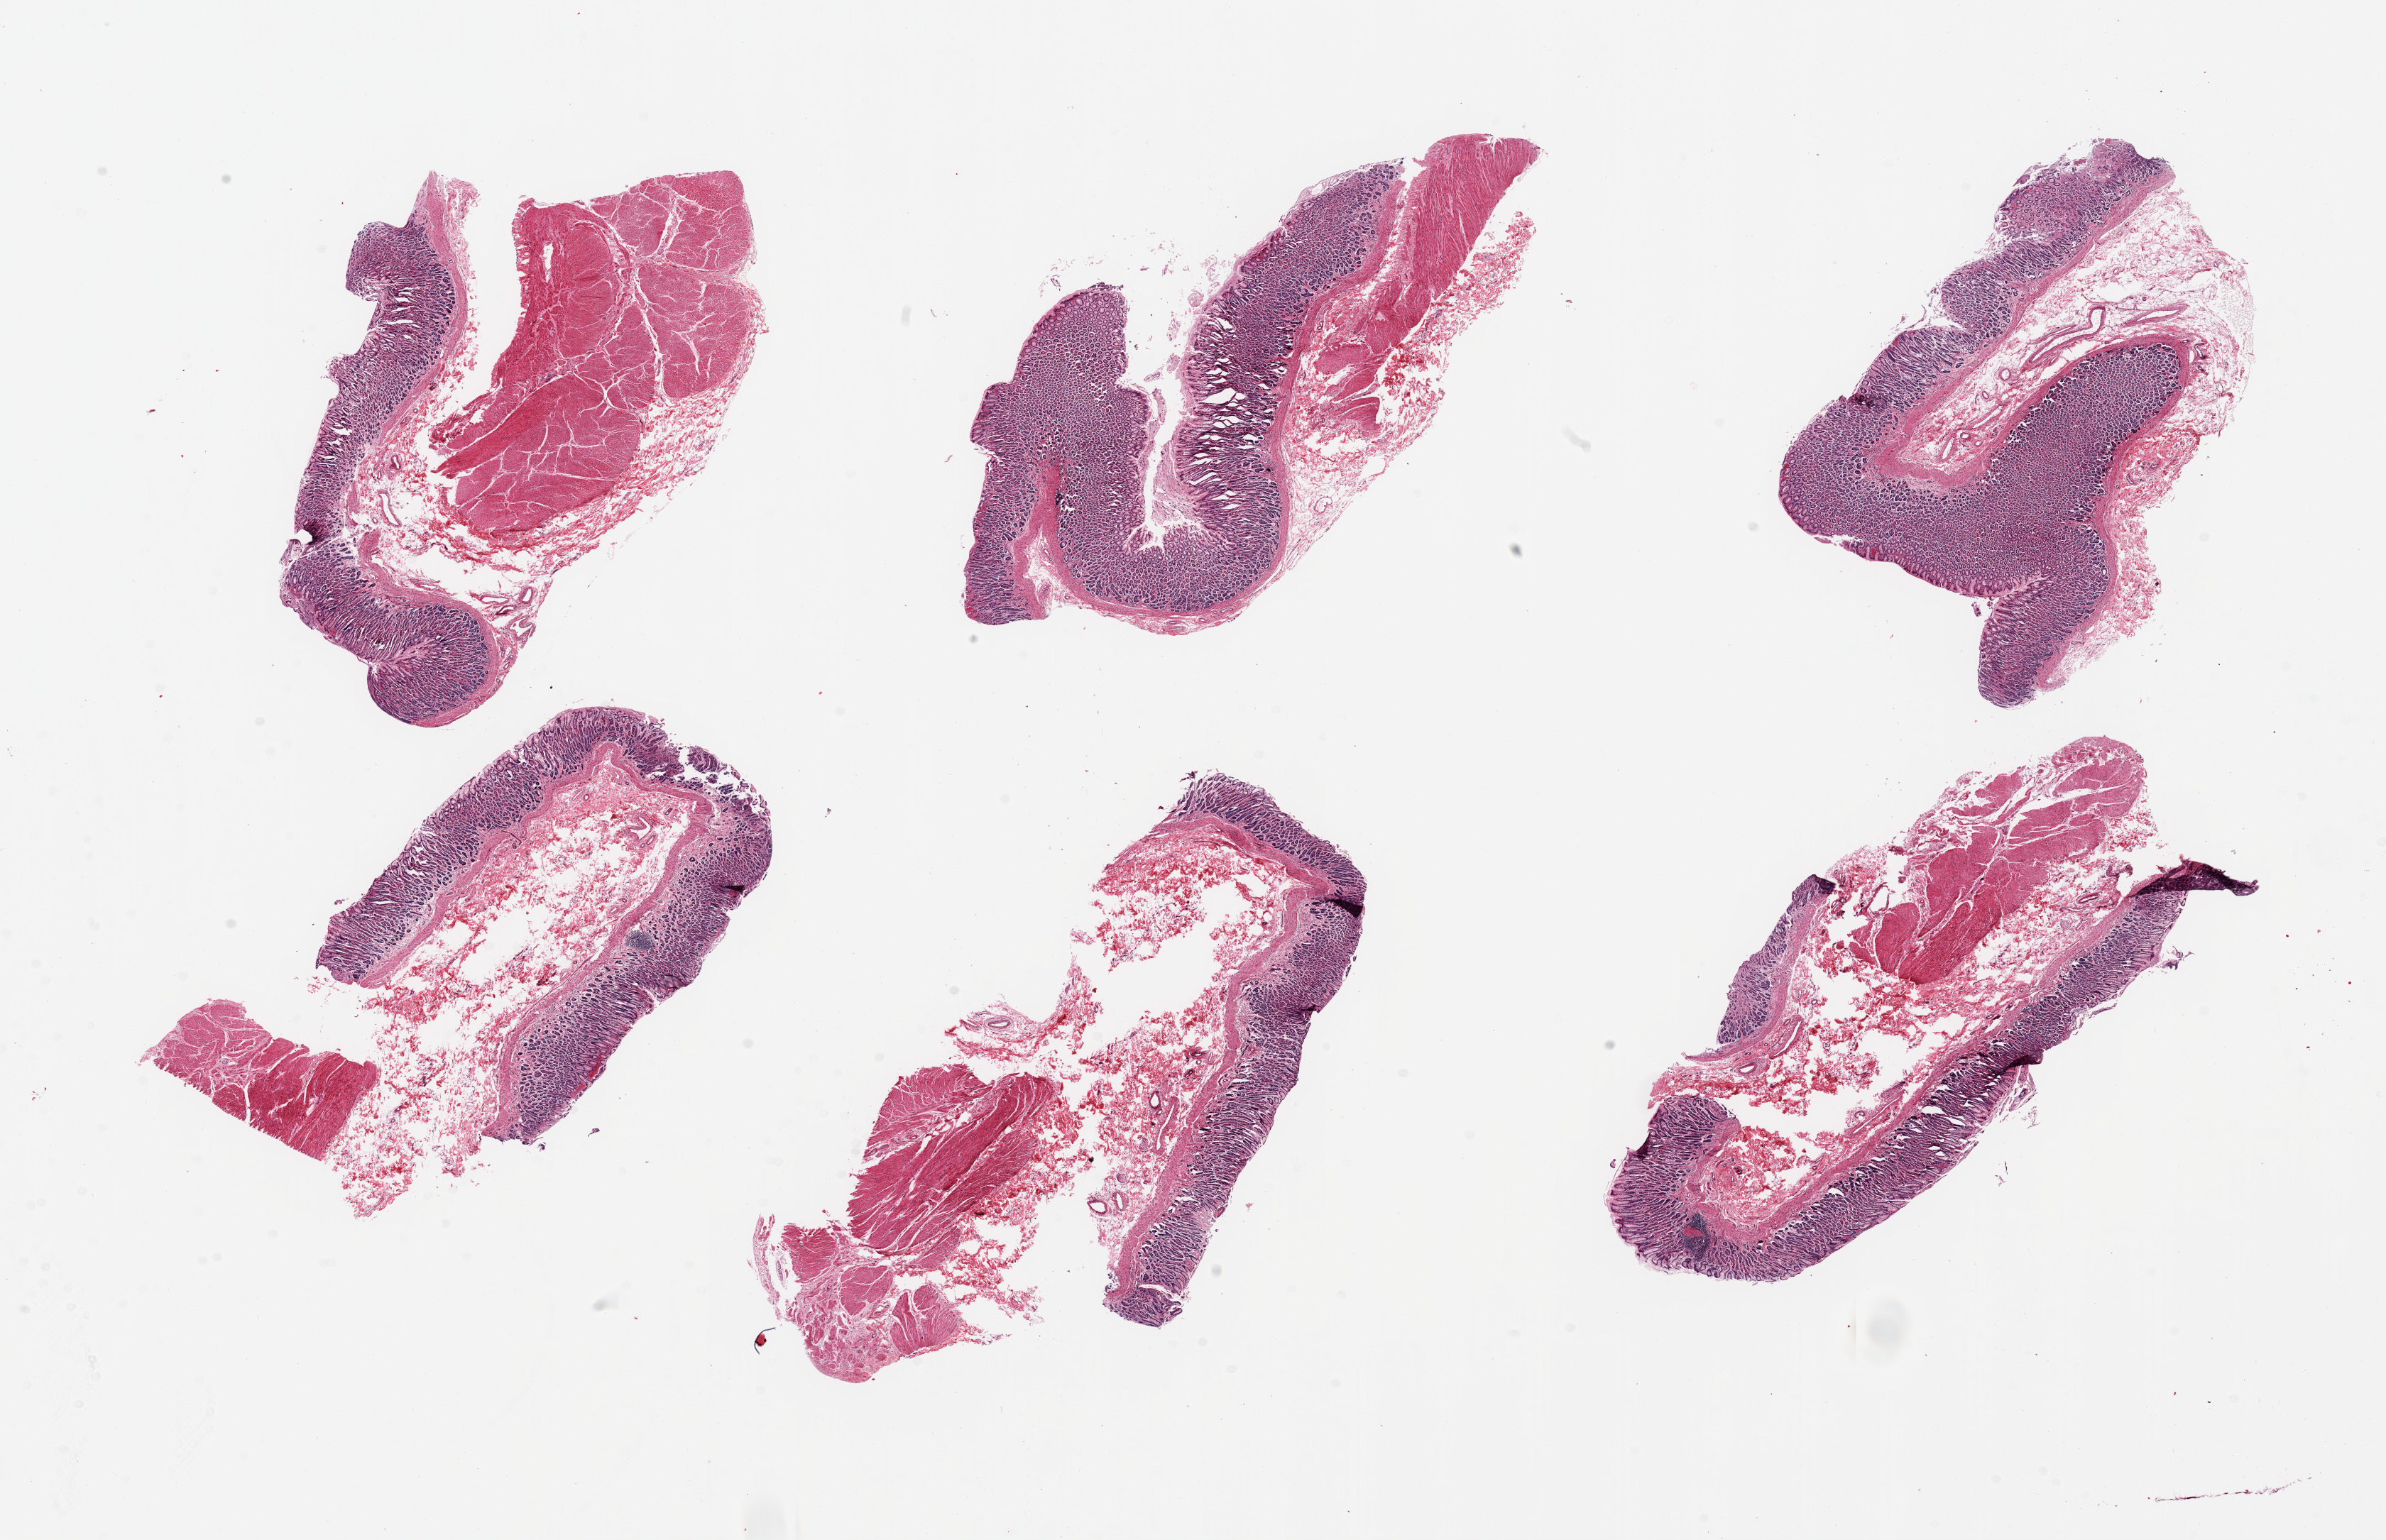
Digitized haematoxylin and eosin-stained section — a low-resolution overview of the entire scanned area, about 26.6 x 17.2 mm. PAXgene-fixed, paraffin-embedded tissue. Section of stomach (target tissue). Donor tissue sample. Male donor.
Review note (as recorded): 6 pieces; possible fixation artifacts; 1 piece has no muscularis.